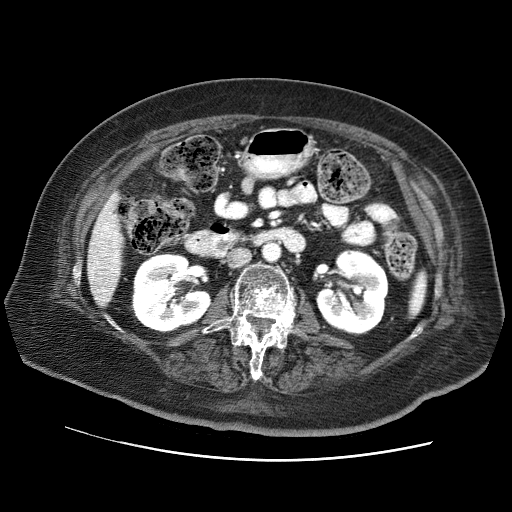
Contrast-enhanced abdominal CT (liver protocol), one axial slice. Slice 20 of 73 in the series (ordered by position). Reconstruction kernel STANDARD. 120 kVp. Soft-tissue window (W 400 / L 40 HU). 512 × 512 image matrix, field of view 380 × 380 mm. Case-level facts recorded for this patient, not image findings: diagnosis: hepatocellular carcinoma (patient treated with transarterial chemoembolisation; whether this scan precedes or follows treatment is not stated here); TNM stage (as recorded): Stage-I; Child-Pugh class: A; tumour nodularity: uninodular.
Outlined on this slice (semi-automatically segmented with operator editing):
- liver parenchyma outside the tumour (the mass and vessels are separate outlines, so this box may not span the whole liver): bounding box [x1, y1, x2, y2] px = [86, 192, 124, 306]
- liver vessels: [93, 225, 118, 293]